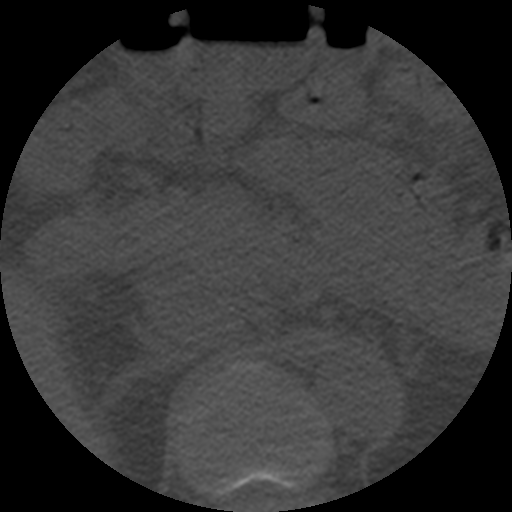
CT including the spine, one axial slice; slice 229 of 508 in the series (ordered by position); reconstruction kernel STANDARD; 120 kVp; bone window (W 1800 / L 400 HU); 1.25 mm slice thickness; 512 × 512 image matrix. Patient age 57 years. From the clinical record (not read from this slice): primary cancer: prostate.
Structures marked on this image (semi-automatic segmentation, software-assisted and operator-edited):
- T11 vertebra: bounding box [x1, y1, x2, y2] px = [214, 463, 319, 496]
- T12 vertebra: [234, 364, 260, 372]